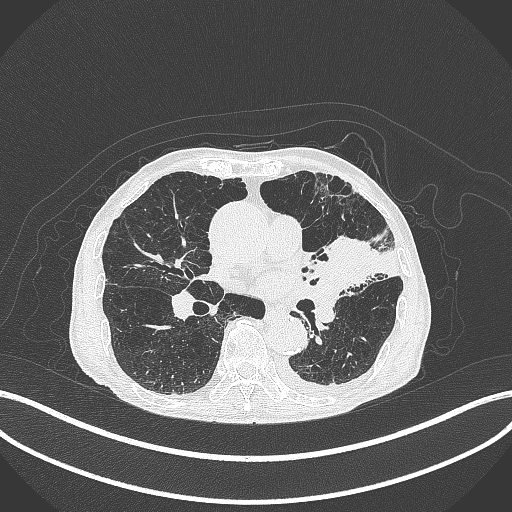
Chest CT, one axial slice; position 196 of 385 along the scan axis; lung window (W 1500 / L -600 HU); 512 × 512 image matrix, field of view 400 × 400 mm. Male patient, age 90 years or older. Case-level facts recorded for this patient, not image findings: clinical TNM (as recorded): T2b N1 M0.
Outlined on this slice (rectangle marked by the reading radiologist):
- lung tumour (recorded histology: squamous cell carcinoma): bounding box <322,231,380,289> (left, top, right, bottom; pixels)